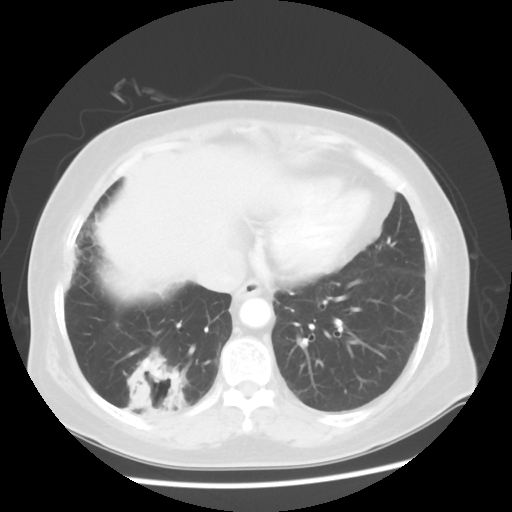
Chest CT, one axial slice; position 17 of 56 along the scan axis; reconstruction kernel STANDARD; 120 kVp; lung window (W 1500 / L -600 HU); 512 × 512 image matrix. Female patient, age 64 years. Case-level facts recorded for this patient, not image findings: clinical TNM (as recorded): Tis N0 M0.
Structures marked on this image (bounding box drawn by a radiologist):
- lung tumour (recorded histology: adenocarcinoma): bounding box [x1, y1, x2, y2] px = [119, 351, 196, 439]